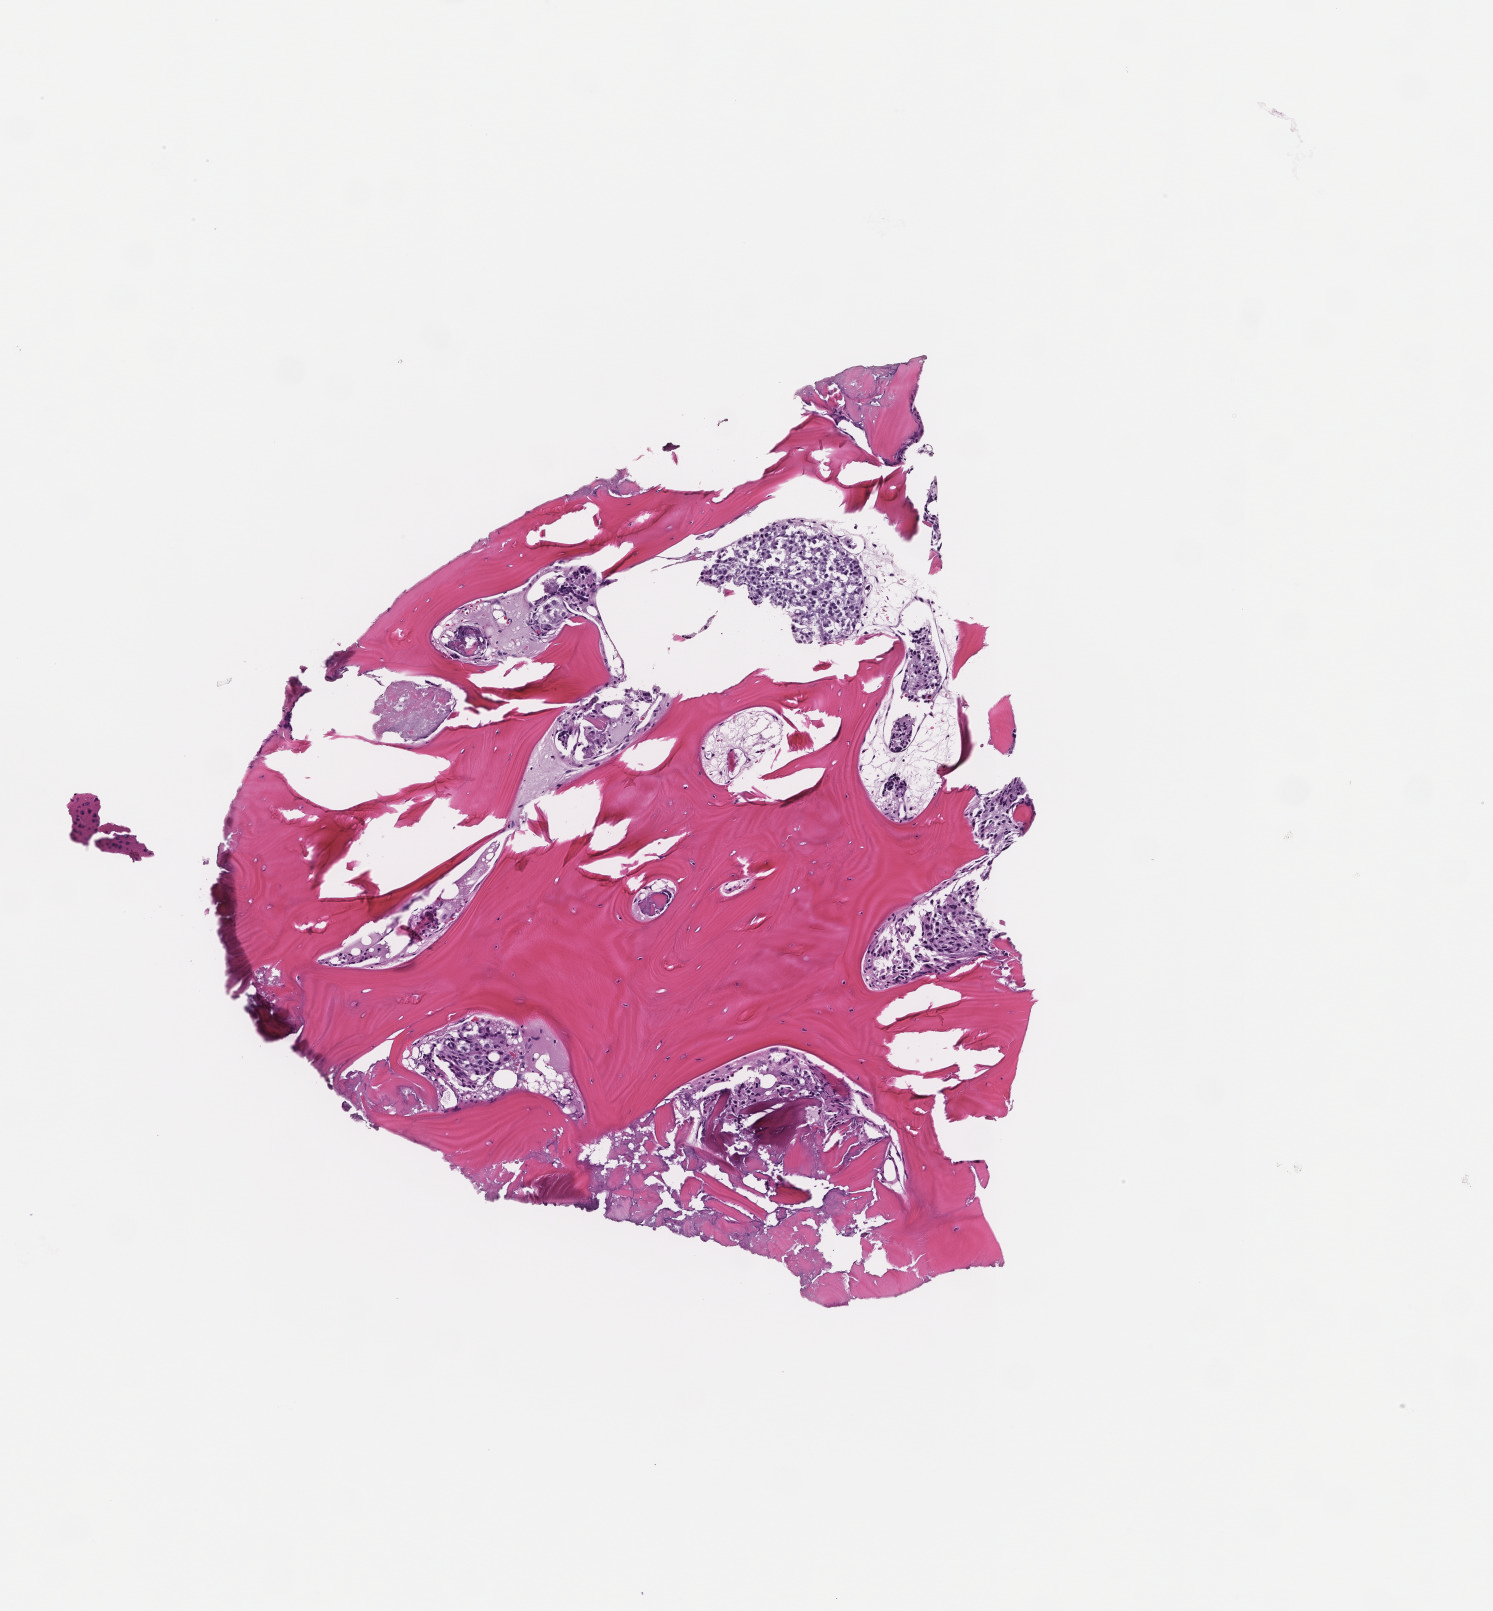
Hematoxylin and eosin (H&E) whole-slide image — low-resolution overview of the scanned area, about 3.0 x 3.3 mm. Formalin-fixed, paraffin-embedded (FFPE) tissue. Male patient.
- this section: metastatic tumor tissue
- patient diagnosis (primary): Prostate Carcinoma